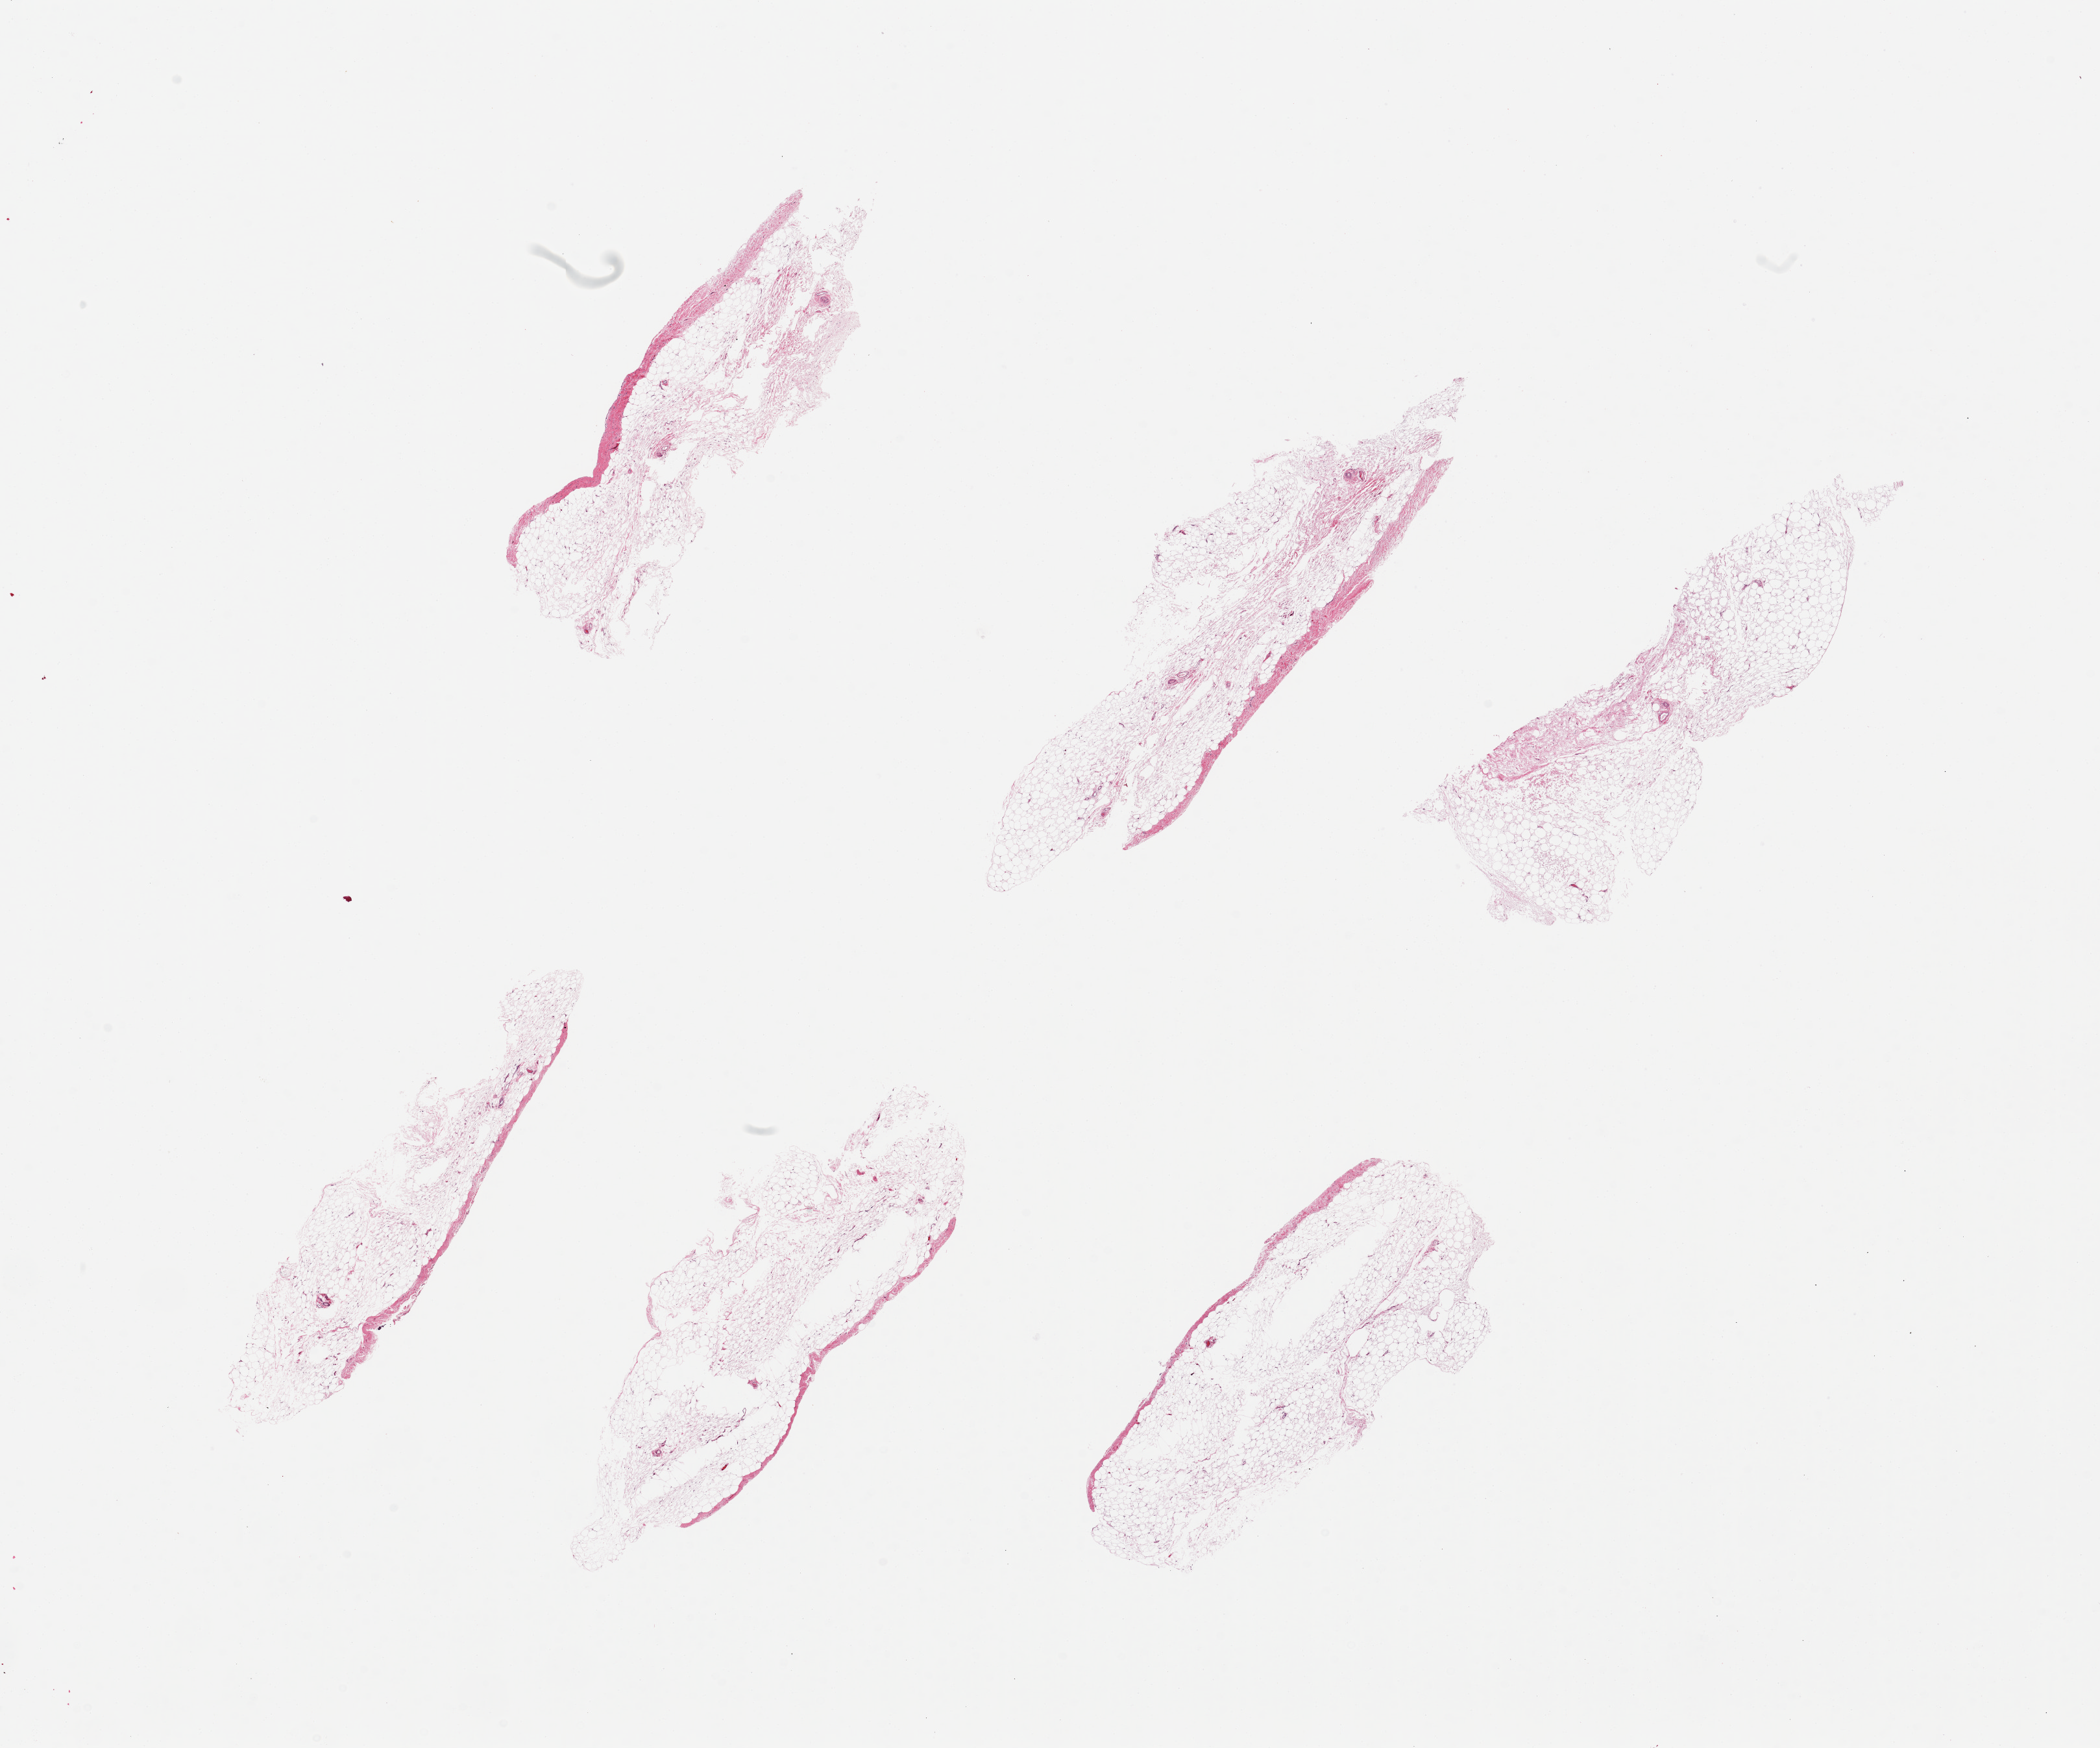
Whole-slide image, hematoxylin and eosin (H&E) stain, brightfield, low-resolution overview of the scanned area, about 25.6 x 21.3 mm, PAXgene-fixed, paraffin-embedded tissue, sampled site (target tissue): urinary bladder, donor tissue sample. Male donor.
Pathologist's review note for this sample: 6 pieces, up to 8x2mm; only adipose and a fibrous border; no muscle or mucosa.